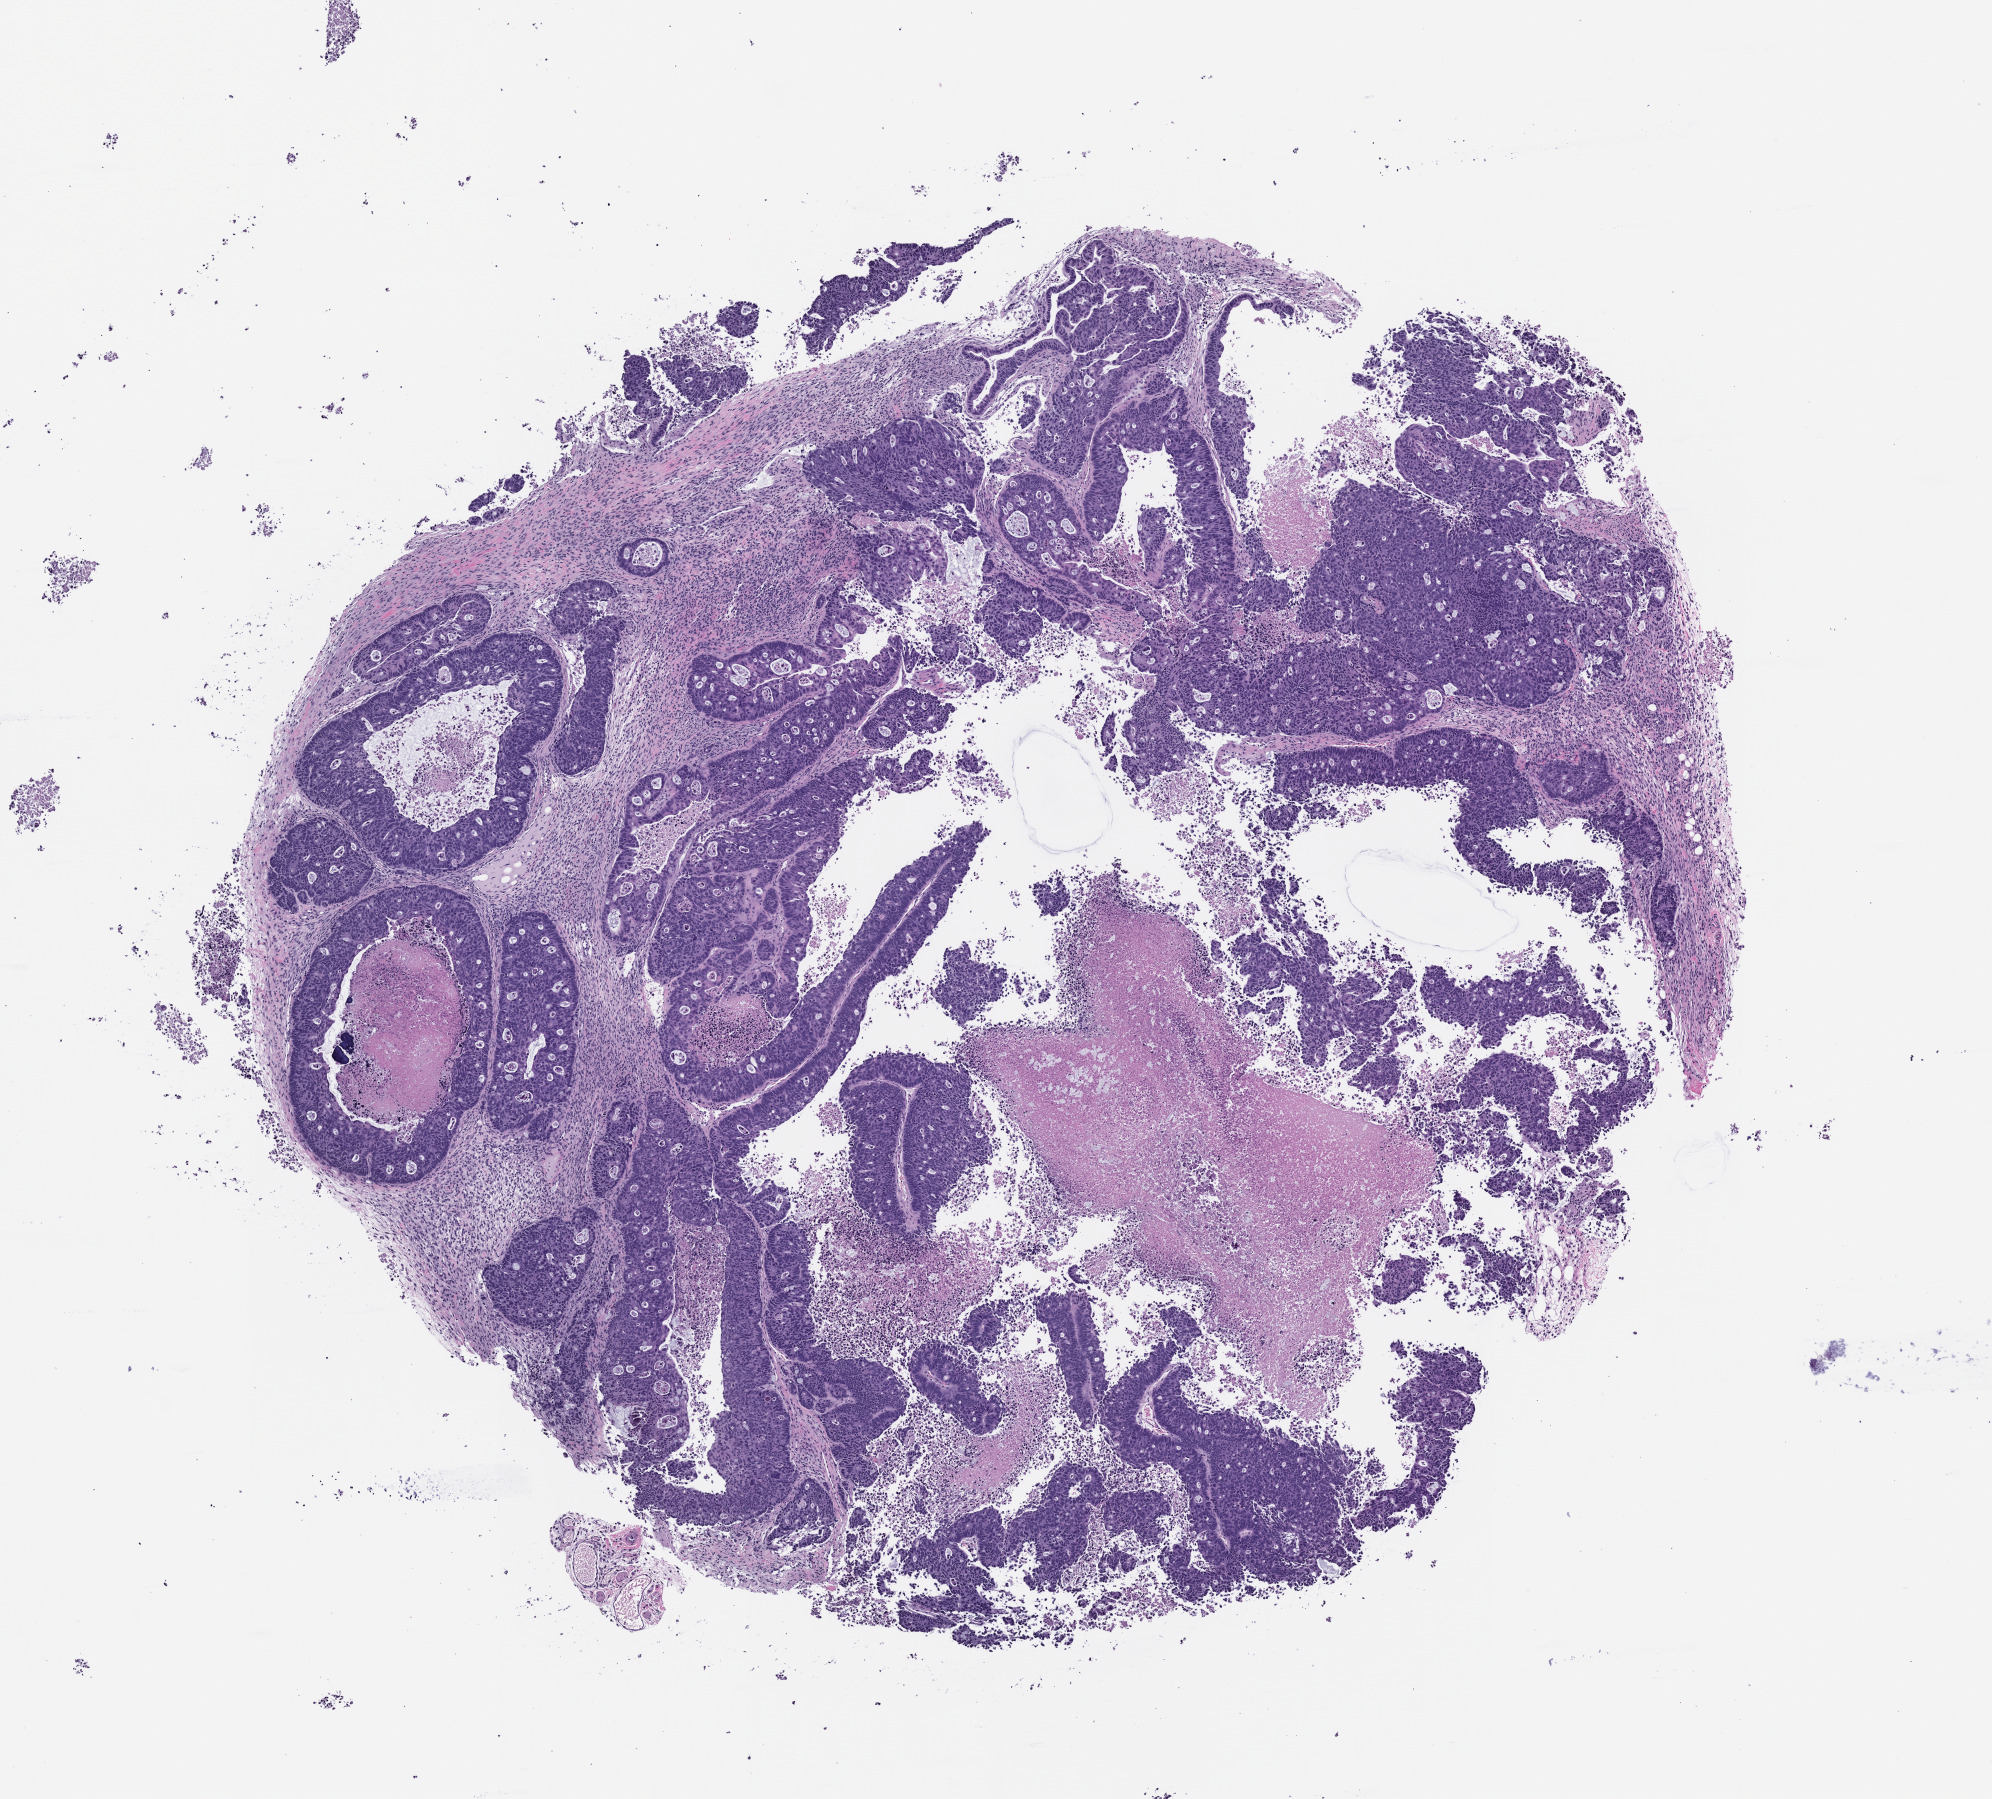
Whole-slide image, H&E: patient-derived xenograft (human tumor grown in a mouse), passage 1, a low-resolution overview of the entire scanned area, about 8.0 x 7.2 mm. Formalin-fixed, paraffin-embedded (FFPE) tissue. Originating tumor site category: rectum.
• originating patient diagnosis: Rectal Adenocarcinoma